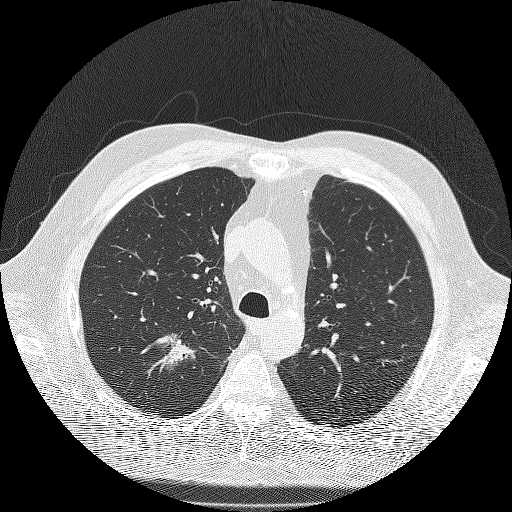
Low-dose screening chest CT, one axial slice; position 141 of 180 along the scan axis; lung window (W 1500 / L -600 HU); 512 × 512 image matrix, field of view 385 × 385 mm.
Annotated regions visible in this slice (expert manual segmentation):
- lesion 1 (tumor, upper lobe of right lung): bounding box <156,334,194,367> (left, top, right, bottom; pixels)